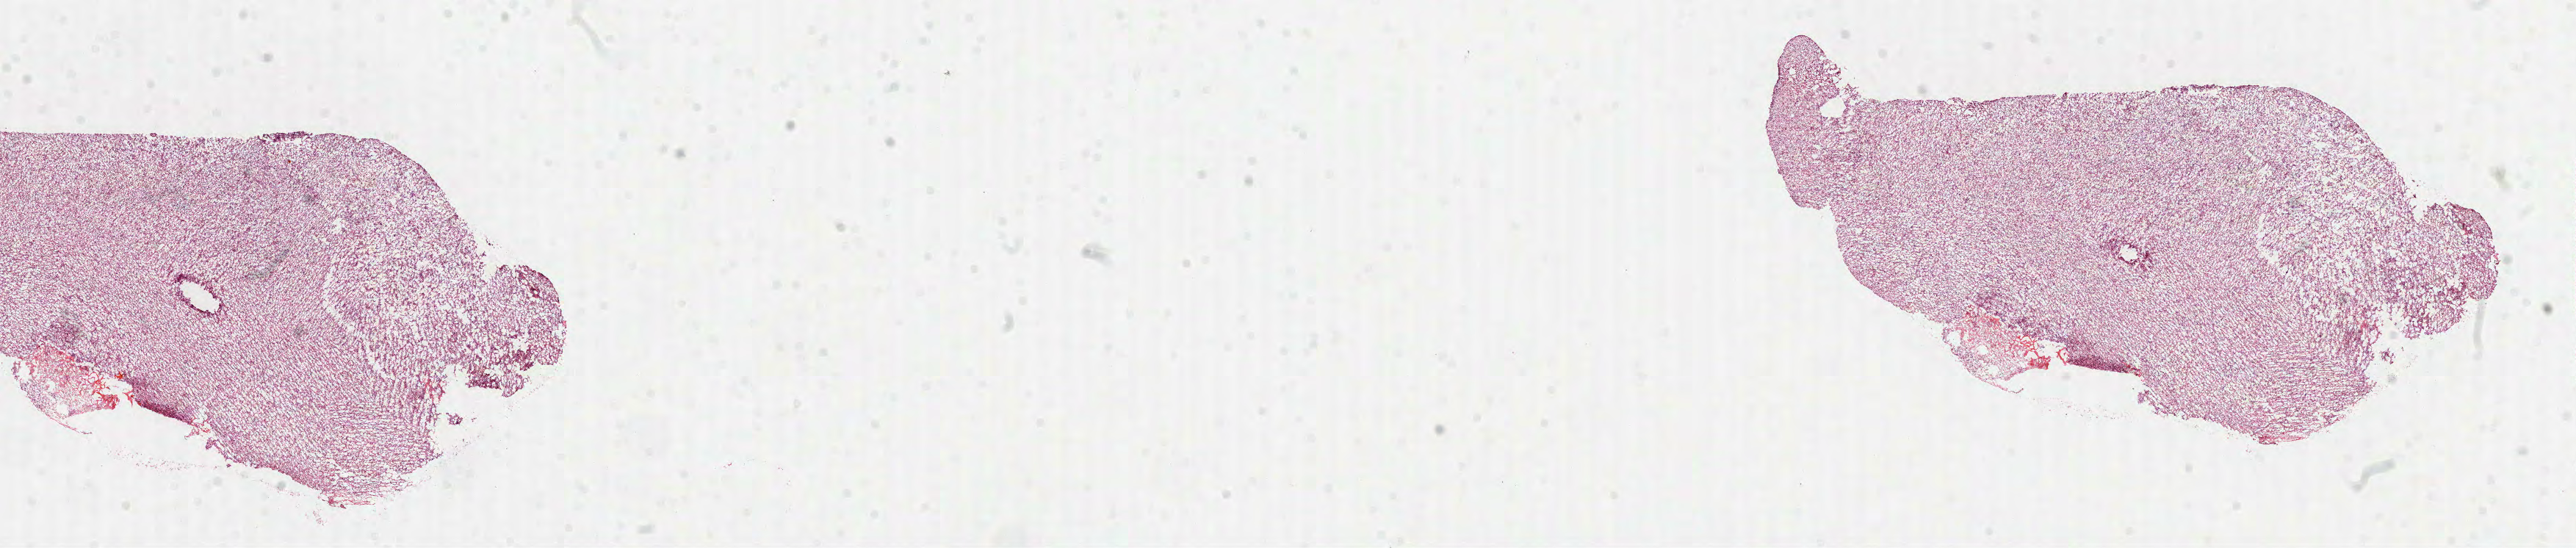
Whole-slide histology image, Hematoxylin and eosin (H&E) stained — a low-resolution overview of the entire scanned area, about 28.3 x 6.0 mm (acquisition: 40x scan), formalin-fixed paraffin-embedded (FFPE) diagnostic section, primary tumour sample from the brain. Patient: female, age at initial diagnosis 68 years.
• histologic diagnosis: Glioblastoma